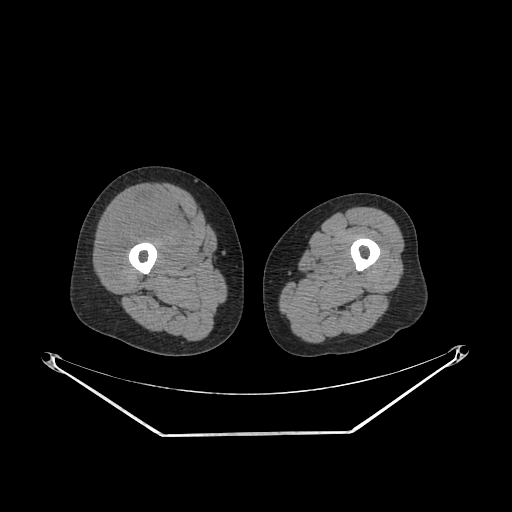
CT of an extremity soft-tissue mass (from a PET/CT study), one axial slice. Slice 233 of 311 in the series (ordered by position). Reconstruction kernel SOFT. Soft-tissue window (W 400 / L 40 HU). 3.75 mm slice thickness. 512 × 512 image matrix, field of view 500 × 500 mm. Female patient. From the clinical record (not read from this slice): histological type: pleiomorphic undifferentiated sarcoma; grade: high; site of the primary tumour: right quadricep.
Annotated regions visible in this slice (expert contour drawn on MRI and transferred to this co-registered scan by the dataset authors):
- tumour plus oedema (research contour): box from (x=100, y=199) to (x=184, y=282) px
- tumour (research contour): (x=100, y=199)–(x=184, y=282)